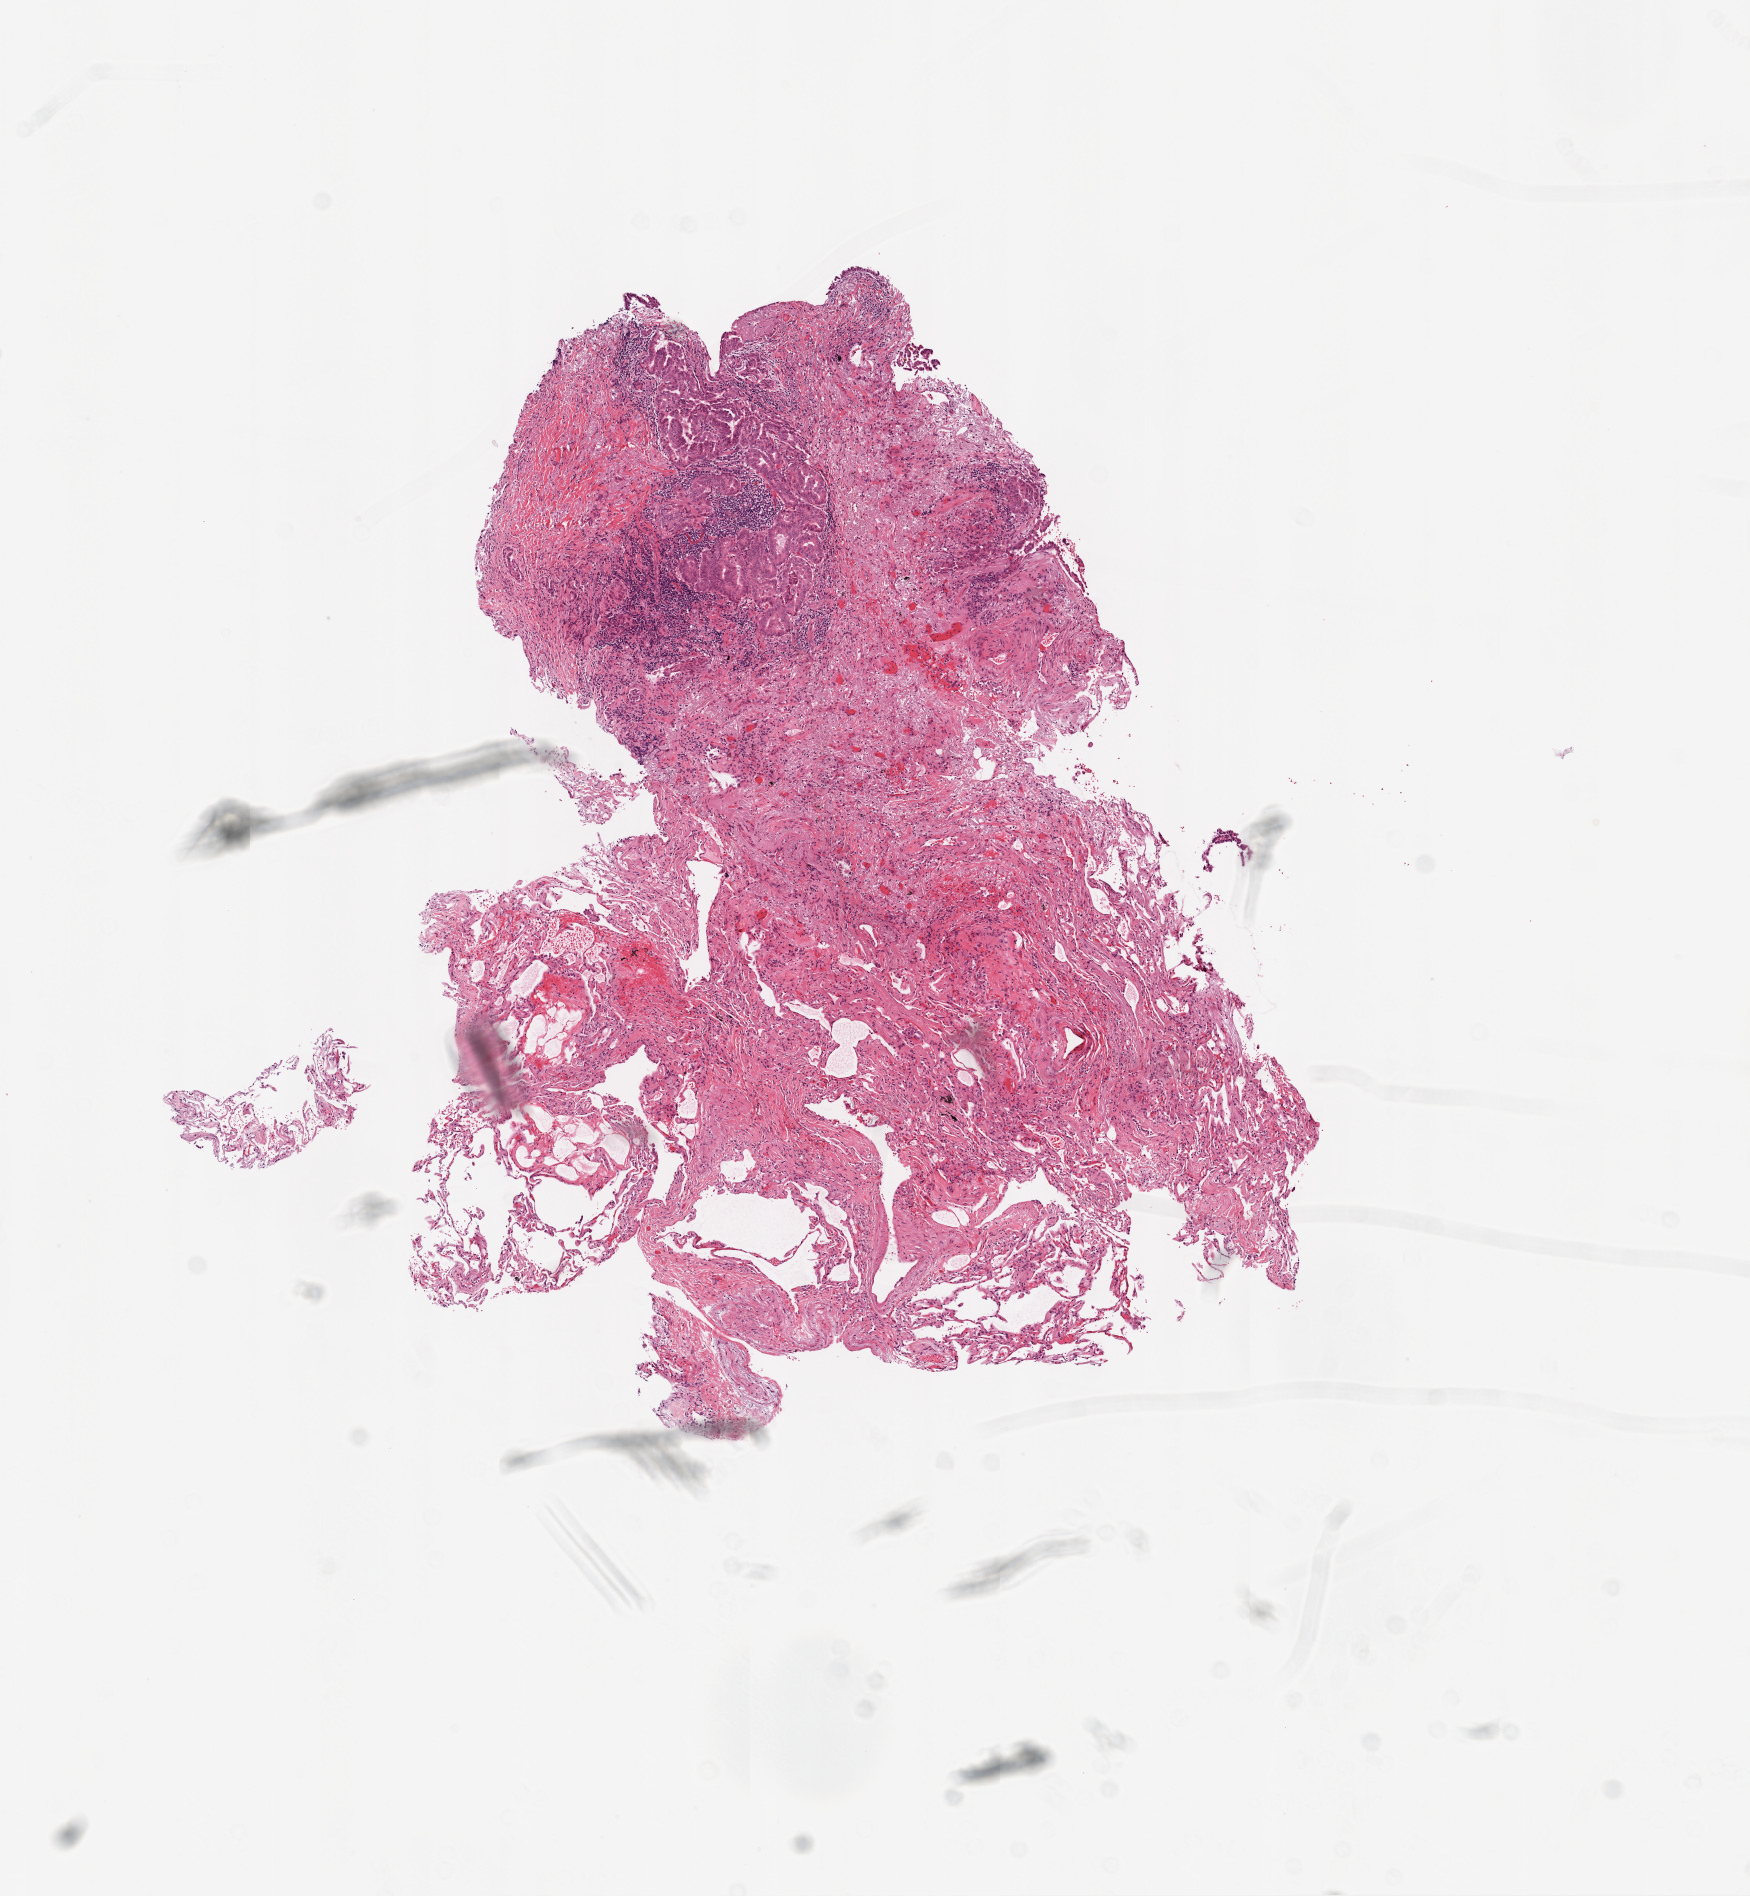
Whole-slide histology image, H&E — shown as a low-resolution overview of the whole scanned area (about 7.0 x 7.6 mm), frozen section from the top of the tissue portion, lung, primary tumour sample. Patient: female, age at initial diagnosis 65 years. Pathologist review of this section (percent, as recorded): tumour cells 15%, tumour nuclei 20%, normal cells 85%, stromal cells 0%, necrosis 0%. Infiltration values recorded for this section: lymphocyte infiltration 10%.
AJCC pathologic stage: IA. Histologic diagnosis: Adenocarcinoma, NOS (upper lobe, lung).